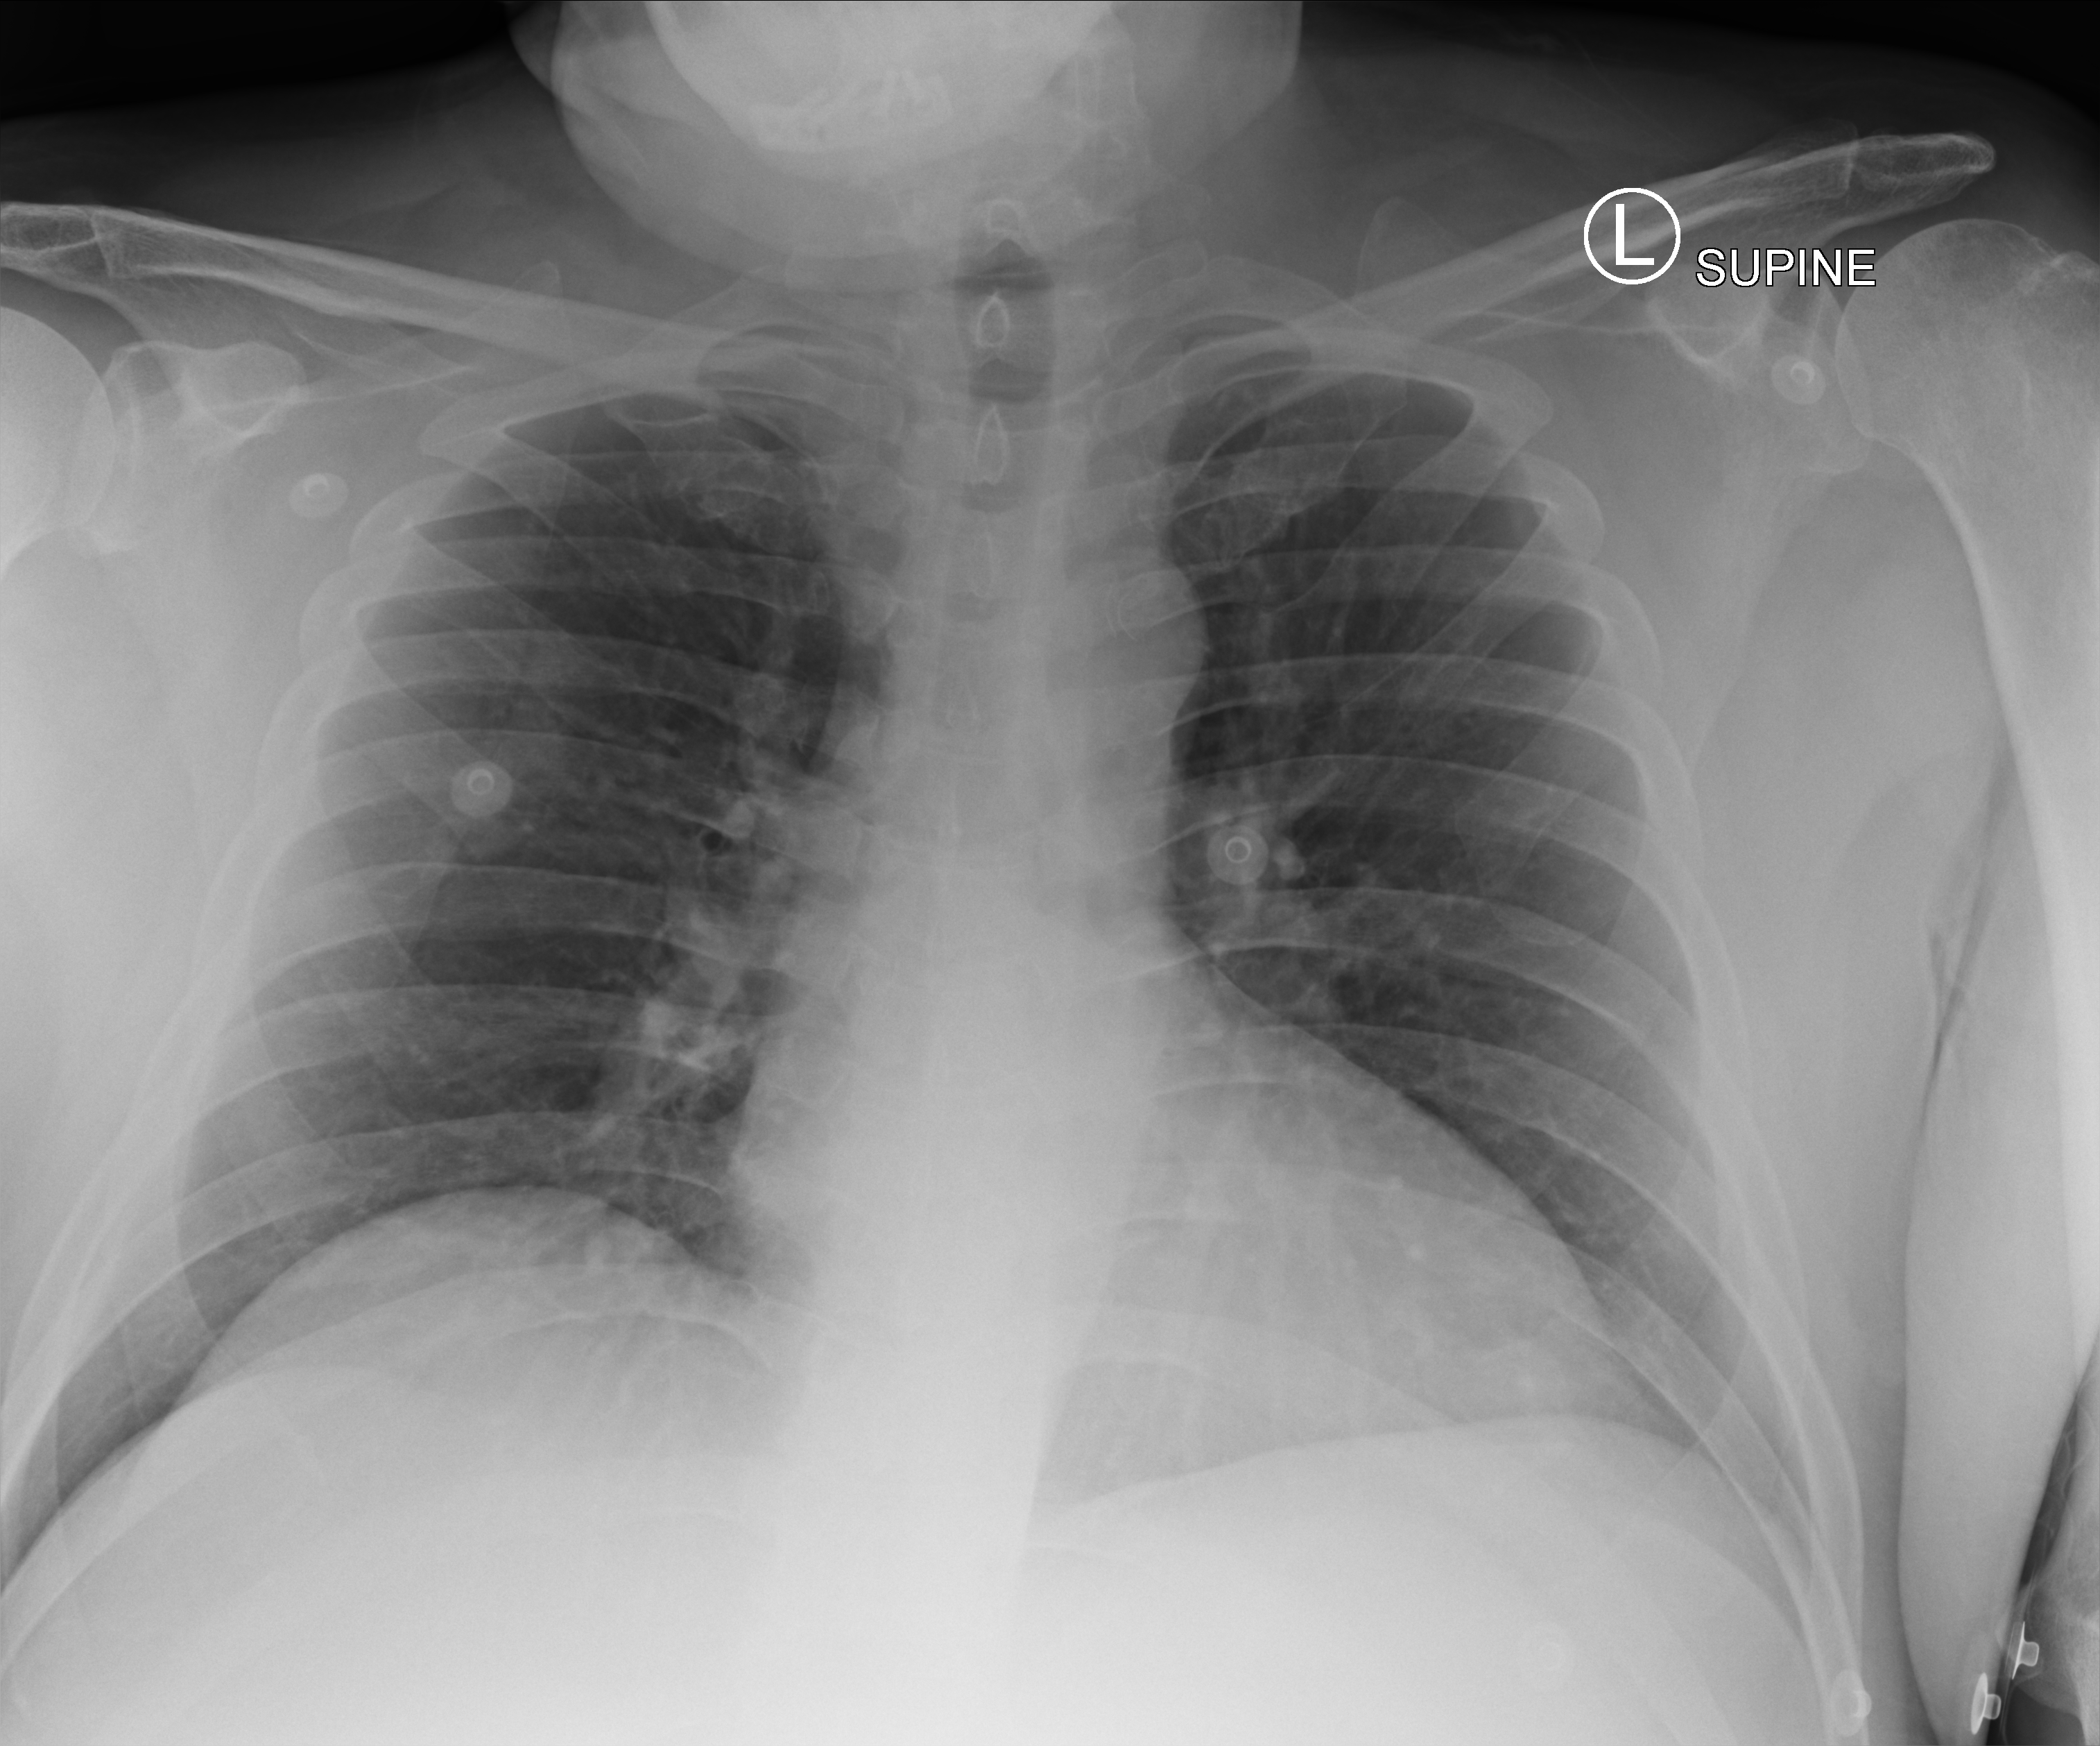
Portable chest radiograph. Male patient hospitalised with COVID-19, age 18–59 years.
From the hospital-stay record, not from the radiograph (when in the stay this image was taken is not recorded): chronic kidney disease (admission record): no.